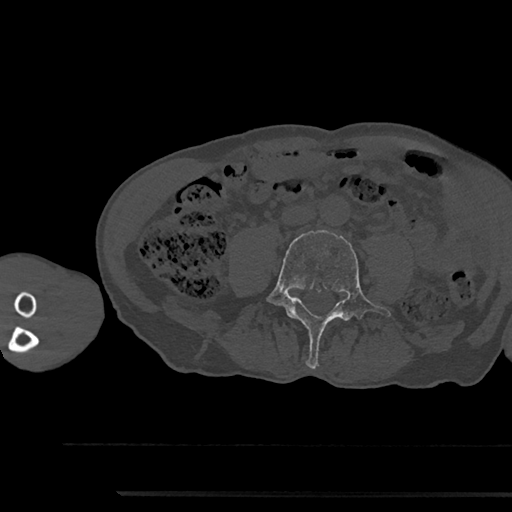
CT including the spine, one axial slice; position 415 of 797 along the scan axis; reconstruction kernel Br40s/3; 120 kVp; bone window (W 1800 / L 400 HU); 0.5 mm slice thickness; 512 × 512 image matrix, field of view 367 × 367 mm. Patient: male, 79 years. From the clinical record (not read from this slice): primary cancer: prostate.
Structures marked on this image (semi-automatic segmentation, software-assisted and operator-edited):
- L4 vertebra: bounding box (x1, y1, x2, y2) in pixels: (267, 230, 392, 369)